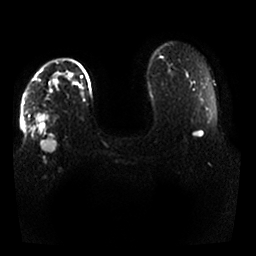
Breast MRI, one axial slice. Position 22 of 25 along the scan axis. Diffusion-weighted series; image 2 of 4 stored at this slice position (different b-values; order by instance number). 1.5 T. 256 × 256 image matrix. Female patient.
Structures marked on this image (manually delineated by an expert):
- tumour on diffusion-weighted imaging: box from (x=31, y=73) to (x=76, y=151) px